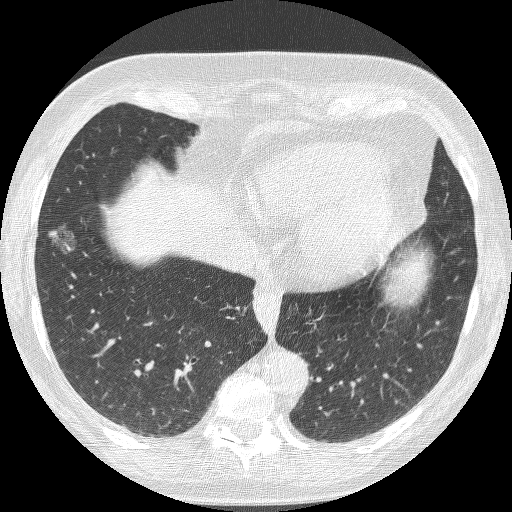
Low-dose screening chest CT, axial slice; baseline screening round; lung window (W 1500 / L -600 HU). Female, age 68 years at enrolment. Current smoker at enrolment.
Expert-annotated lung lesion, box from (x=33, y=222) to (x=85, y=273) px. The exam's reader record, not a measurement of the box and not confirmed to be the same lesion: non-calcified nodule or mass ≥4 mm, right lower lobe, 16 × 12 mm, poorly defined margins, ground glass attenuation. Lung cancer was diagnosed 406 days after this screen (after the second annual screen): bronchiolo-alveolar adenocarcinoma, NOS, right lower lobe, well differentiated (G1), stage IA (AJCC 6th edition), 13 mm at pathology.